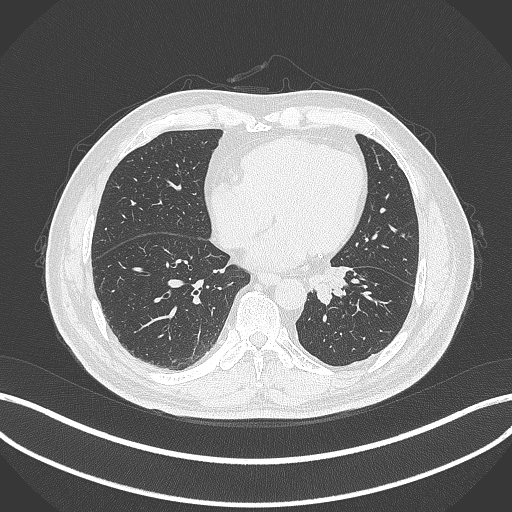
Chest CT, one axial slice. Position 93 of 312 along the scan axis. Reconstruction kernel B70f. Lung window (W 1500 / L -600 HU). 512 × 512 image matrix, field of view 400 × 400 mm. Male patient, age 71 years. Case-level facts recorded for this patient, not image findings: clinical TNM (as recorded): T1b N0 M0.
Structures marked on this image (bounding box drawn by a radiologist):
- lung tumour (recorded histology: squamous cell carcinoma): bounding box (x1, y1, x2, y2) in pixels: (309, 265, 354, 305)